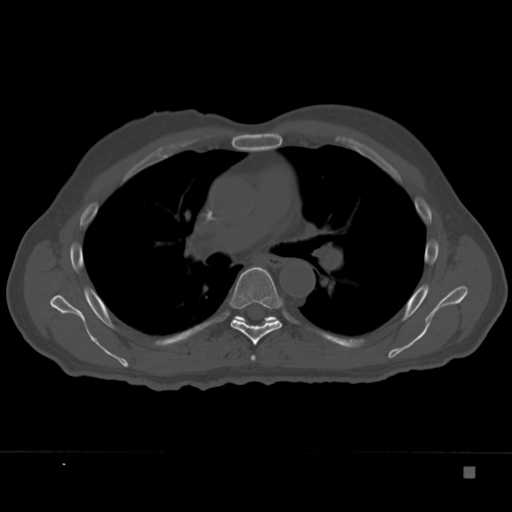
CT including the spine, one axial slice. Position 238 of 332 along the scan axis. Reconstruction kernel Br40s. Bone window (W 1800 / L 400 HU). 1.5 mm slice thickness. 512 × 512 image matrix, field of view 389 × 389 mm. Patient: male, 72 years. From the clinical record (not read from this slice): primary cancer: skeletal.
Annotated regions visible in this slice (semi-automatically segmented with operator editing):
- T5 vertebra: bounding box (x1, y1, x2, y2) in pixels: (251, 355, 256, 361)
- T6 vertebra: (230, 267, 283, 345)
- T7 vertebra: (235, 316, 276, 325)